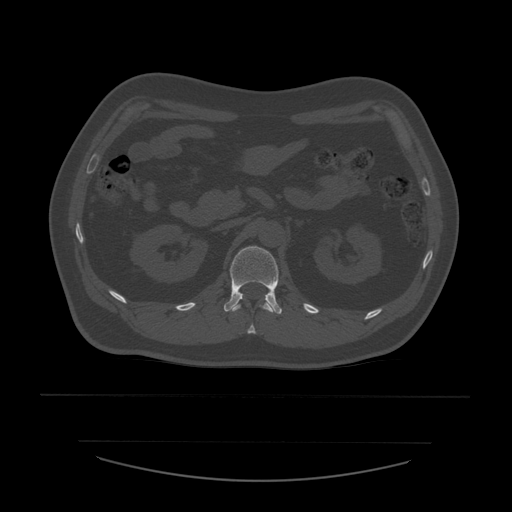
CT including the spine, one axial slice. Slice 234 of 532 in the series (ordered by position). Reconstruction kernel STANDARD. 120 kVp. Bone window (W 1800 / L 400 HU). 1.25 mm slice thickness. 512 × 512 image matrix. Patient age 44 years. Case-level facts recorded for this patient, not image findings: primary cancer: soft tissue sarcoma.
Structures marked on this image (semi-automatic segmentation, software-assisted and operator-edited):
- L1 vertebra: bounding box [x1, y1, x2, y2] px = [224, 246, 282, 315]
- T12 vertebra: [233, 301, 273, 334]